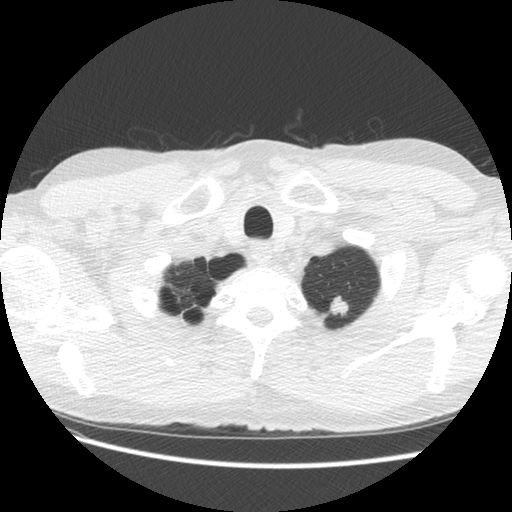
Low-dose screening chest CT, one axial slice; slice 118 of 131 in the series (ordered by position); reconstruction kernel STANDARD; 140 kVp; lung window (W 1500 / L -600 HU); 512 × 512 image matrix, field of view 340 × 340 mm.
Outlined on this slice (manually delineated by an expert):
- lesion 1 (tumor, upper lobe of left lung): bounding box <329,296,349,316> (left, top, right, bottom; pixels)